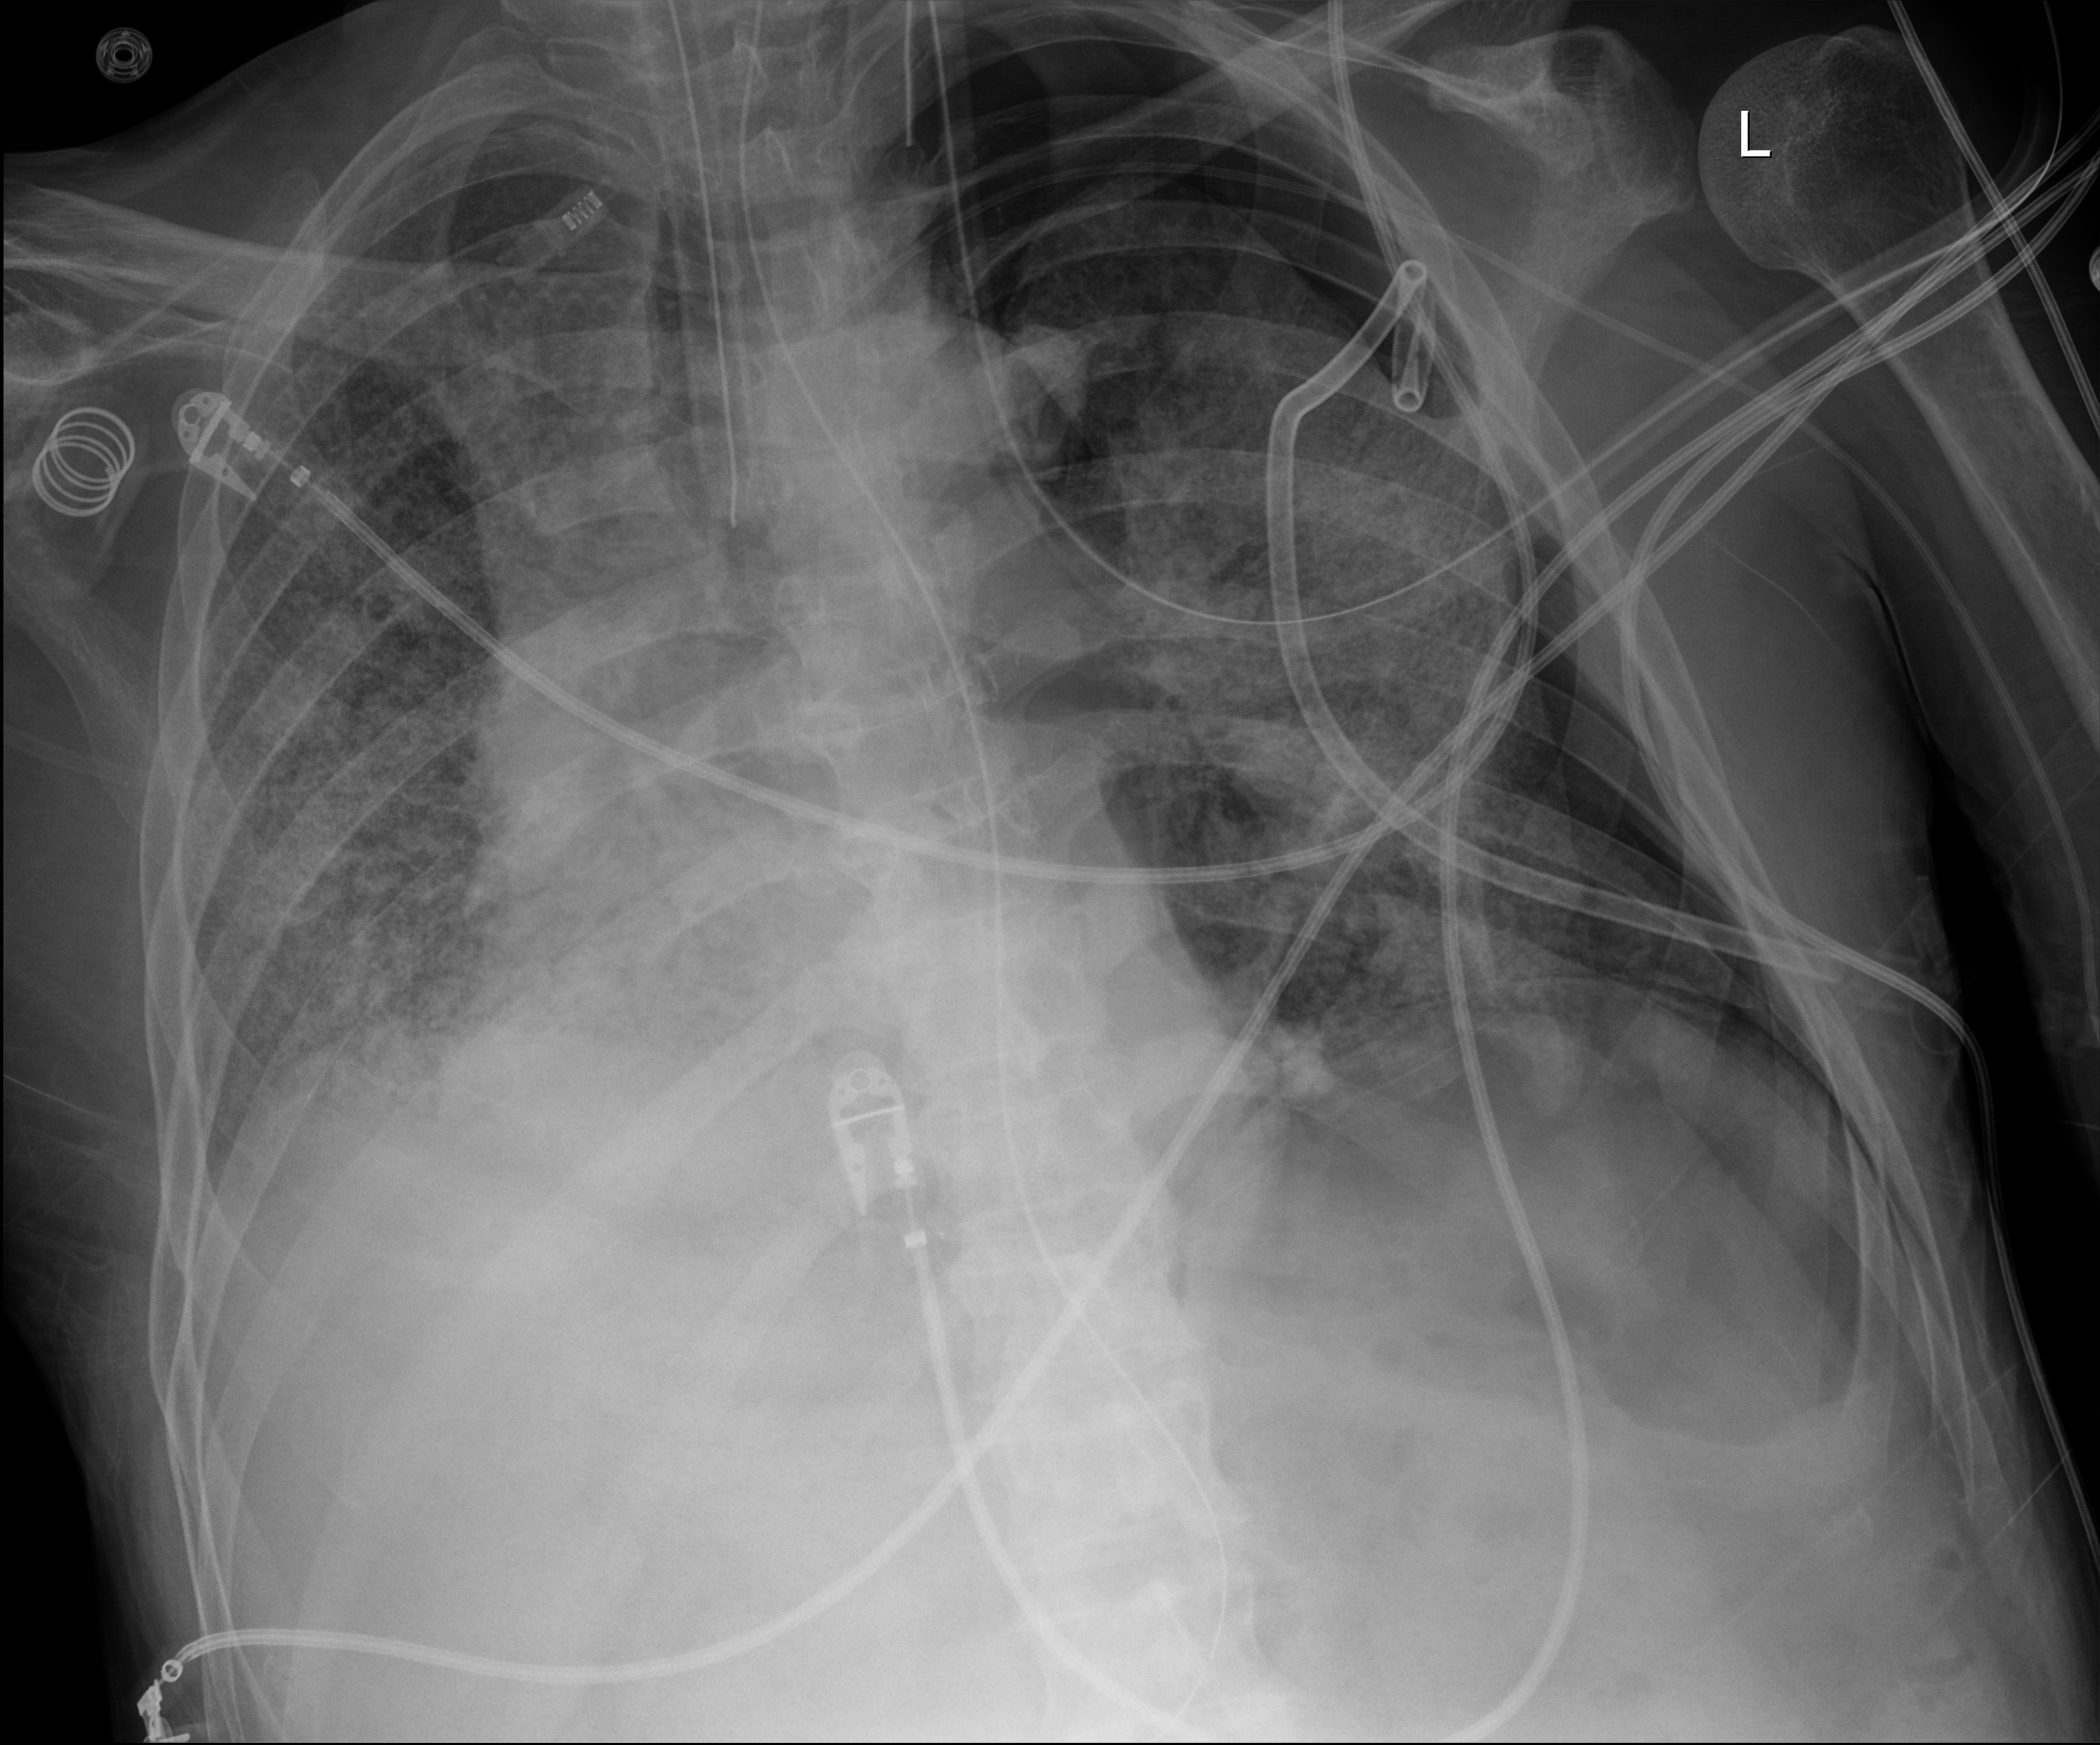
Portable chest radiograph, anteroposterior (AP) projection. Patient hospitalised with COVID-19; male, aged 60–74 years.
Admission-level facts for this patient (not findings on this image; timing relative to this image not recorded):
- admitted to intensive care during this hospital stay: yes
- mechanically ventilated during this hospital stay: yes